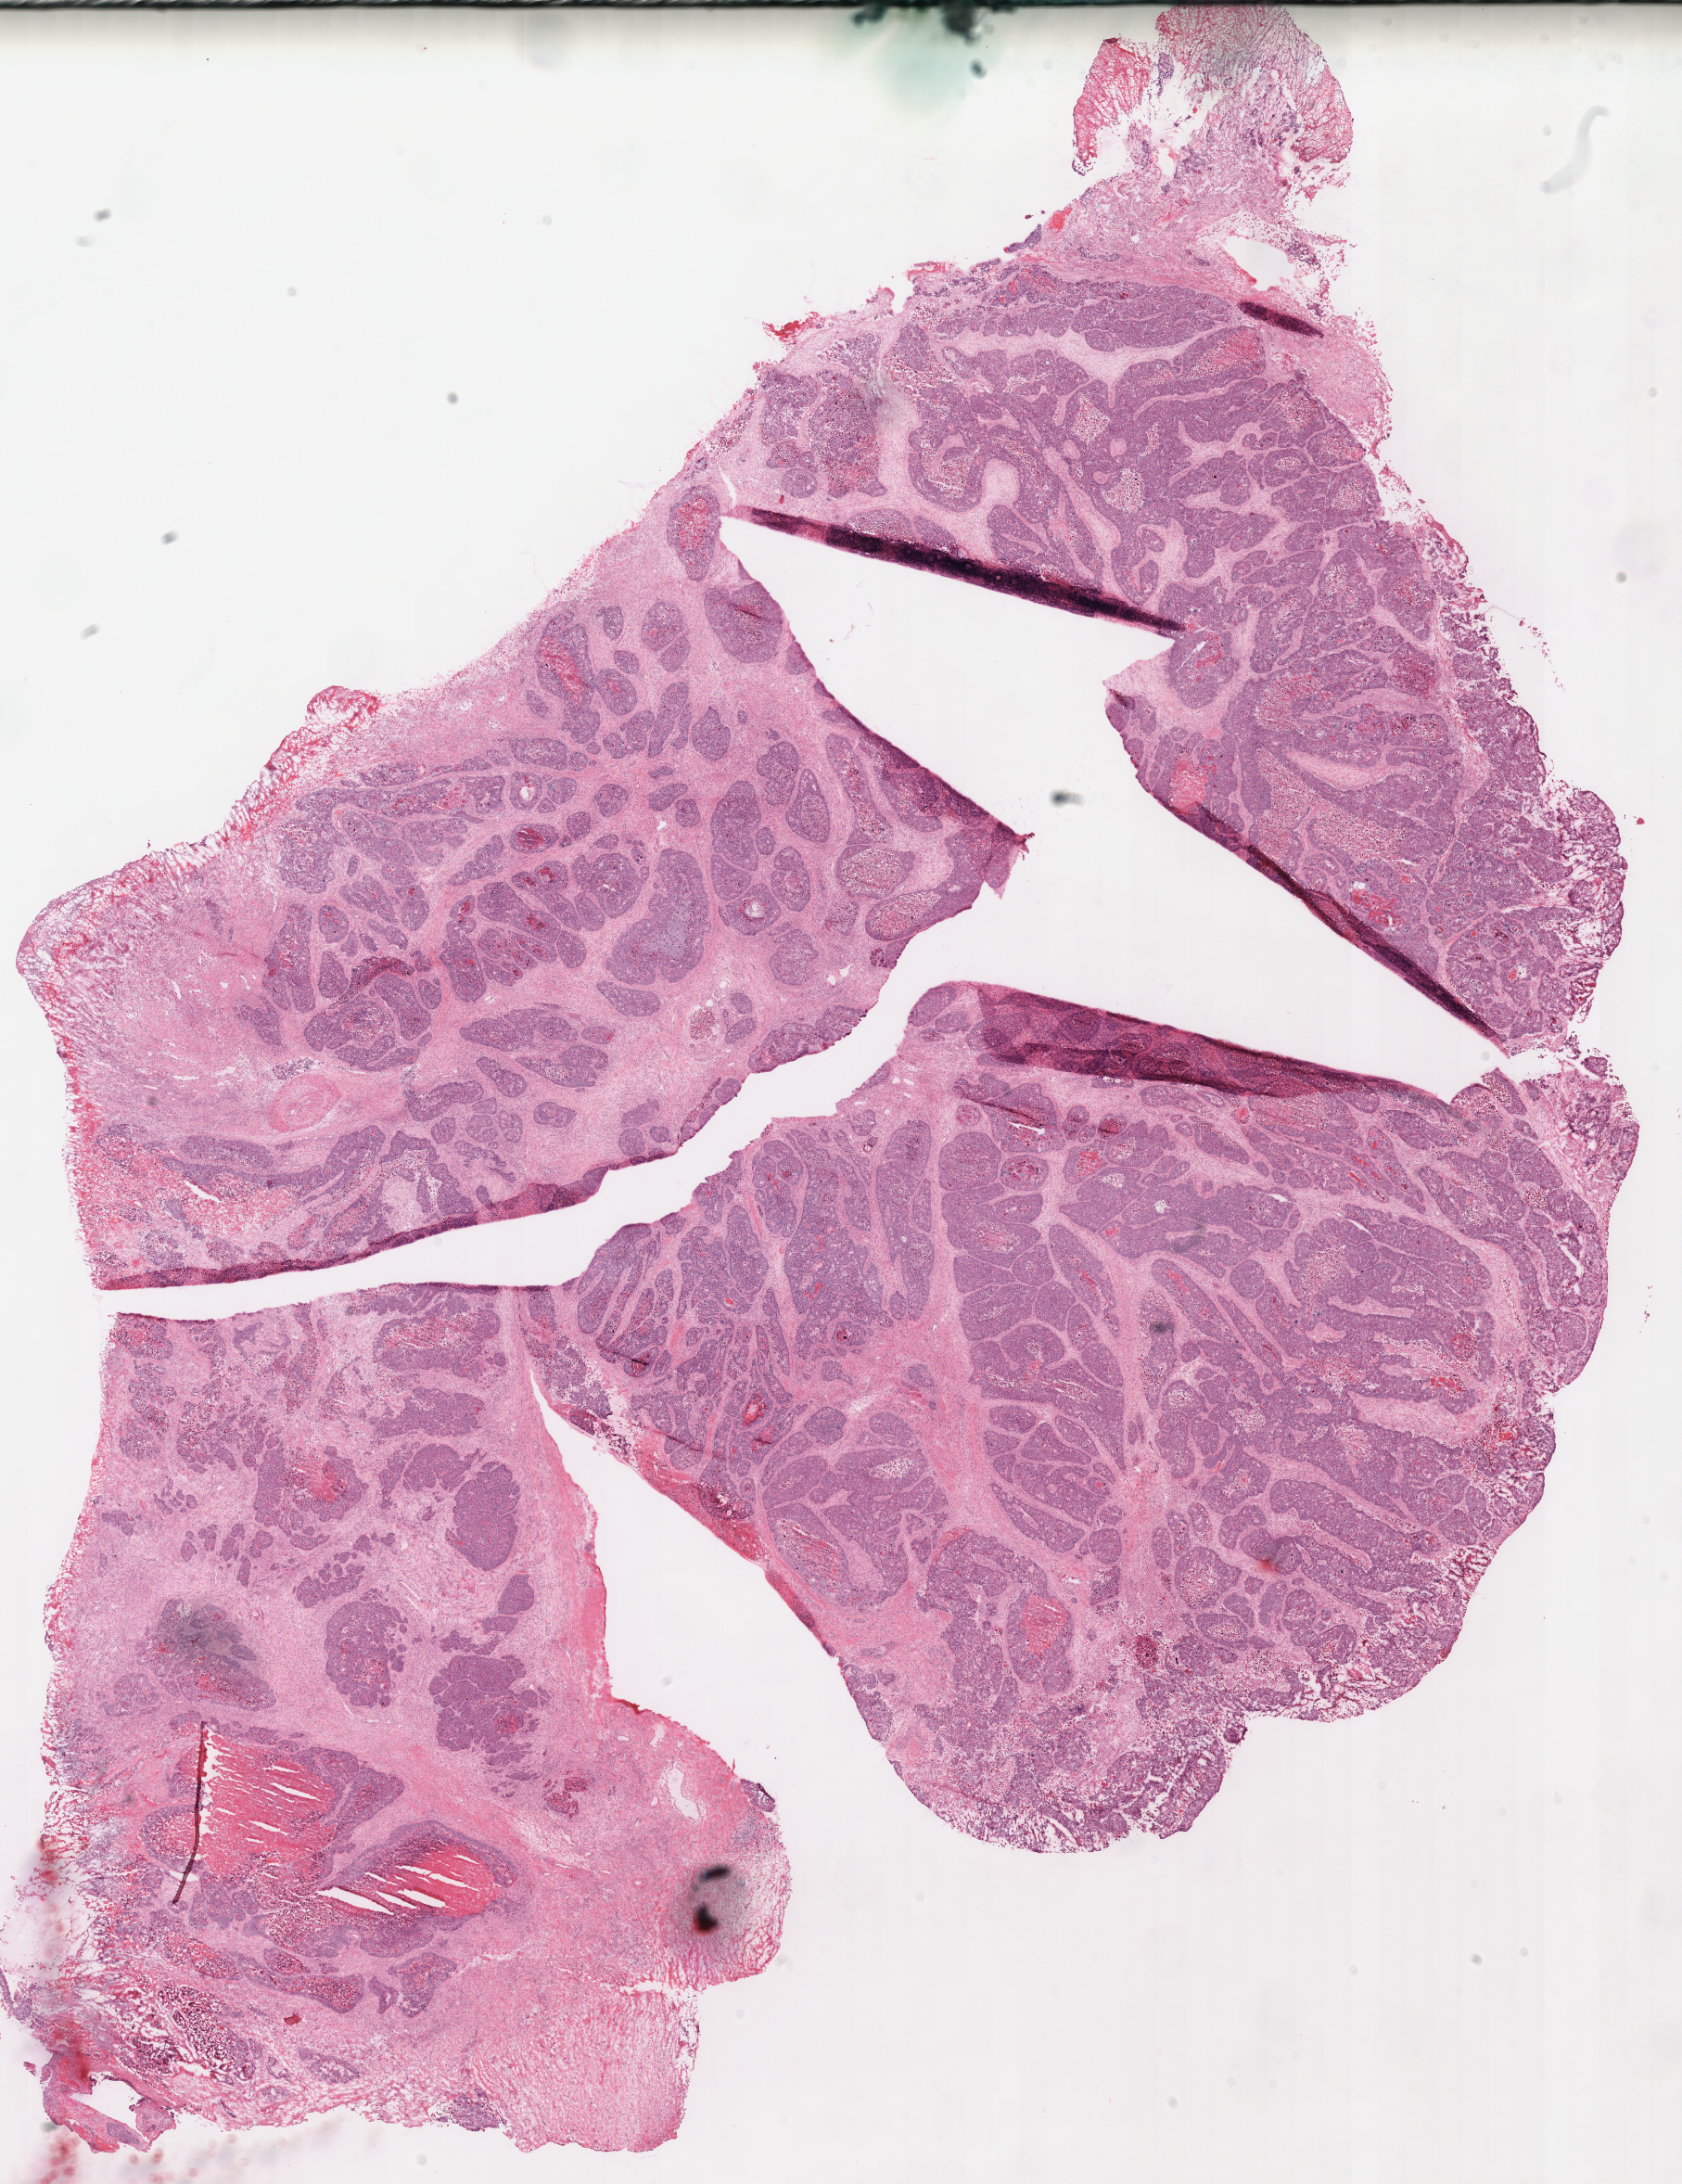
Whole-slide histology image, H&E, whole scanned area (about 14.3 x 18.6 mm, slide scanned at 40x) shown as a low-resolution overview. Frozen section from the top of the tissue portion. Stomach, primary tumour sample. Male patient; age at initial diagnosis 76 years. Histologic grade: G2 (moderately differentiated). Composition of this section per pathologist review: tumour cells 83%, tumour nuclei 85%, normal cells 3%, stromal cells 6%, necrosis 8%. Inflammatory infiltration, as recorded: lymphocyte infiltration 10%, monocyte infiltration 0%, neutrophil infiltration 0%.
• histologic diagnosis: Adenocarcinoma, NOS (fundus of stomach)
• AJCC pathologic stage: IB (7th edition)
• lymph nodes positive (case pathology): 0 of 12 examined